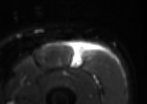
MRI of an extremity soft-tissue mass, one axial slice. Slice 34 of 85 in the series (ordered by position). T2-weighted fat-saturated. MR volume resampled by the dataset authors to the PET/CT grid (not the native acquisition matrix). 147 × 104 image matrix. Male patient. From the clinical record (not read from this slice): histological type: extraskeletal osteosarcoma; grade: high; site of the primary tumour: thigh.
Structures marked on this image (expert contour drawn on MRI and transferred to this co-registered scan by the dataset authors):
- gross tumour volume (mass): bounding box [x1, y1, x2, y2] px = [78, 46, 84, 61]